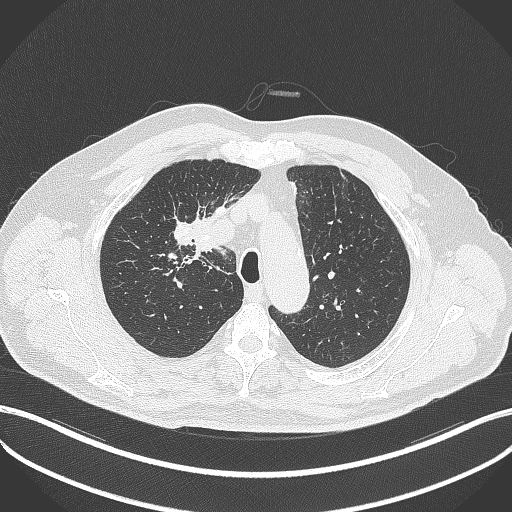
Chest CT, one axial slice. Position 301 of 411 along the scan axis. Lung window (W 1500 / L -600 HU). 1 mm slice thickness. 512 × 512 image matrix. Male patient, age 60 years. Case-level facts recorded for this patient, not image findings: clinical TNM (as recorded): T1b N1 M0.
Structures marked on this image (bounding box drawn by a radiologist):
- lung tumour (recorded histology: squamous cell carcinoma): box from (x=194, y=225) to (x=219, y=262) px